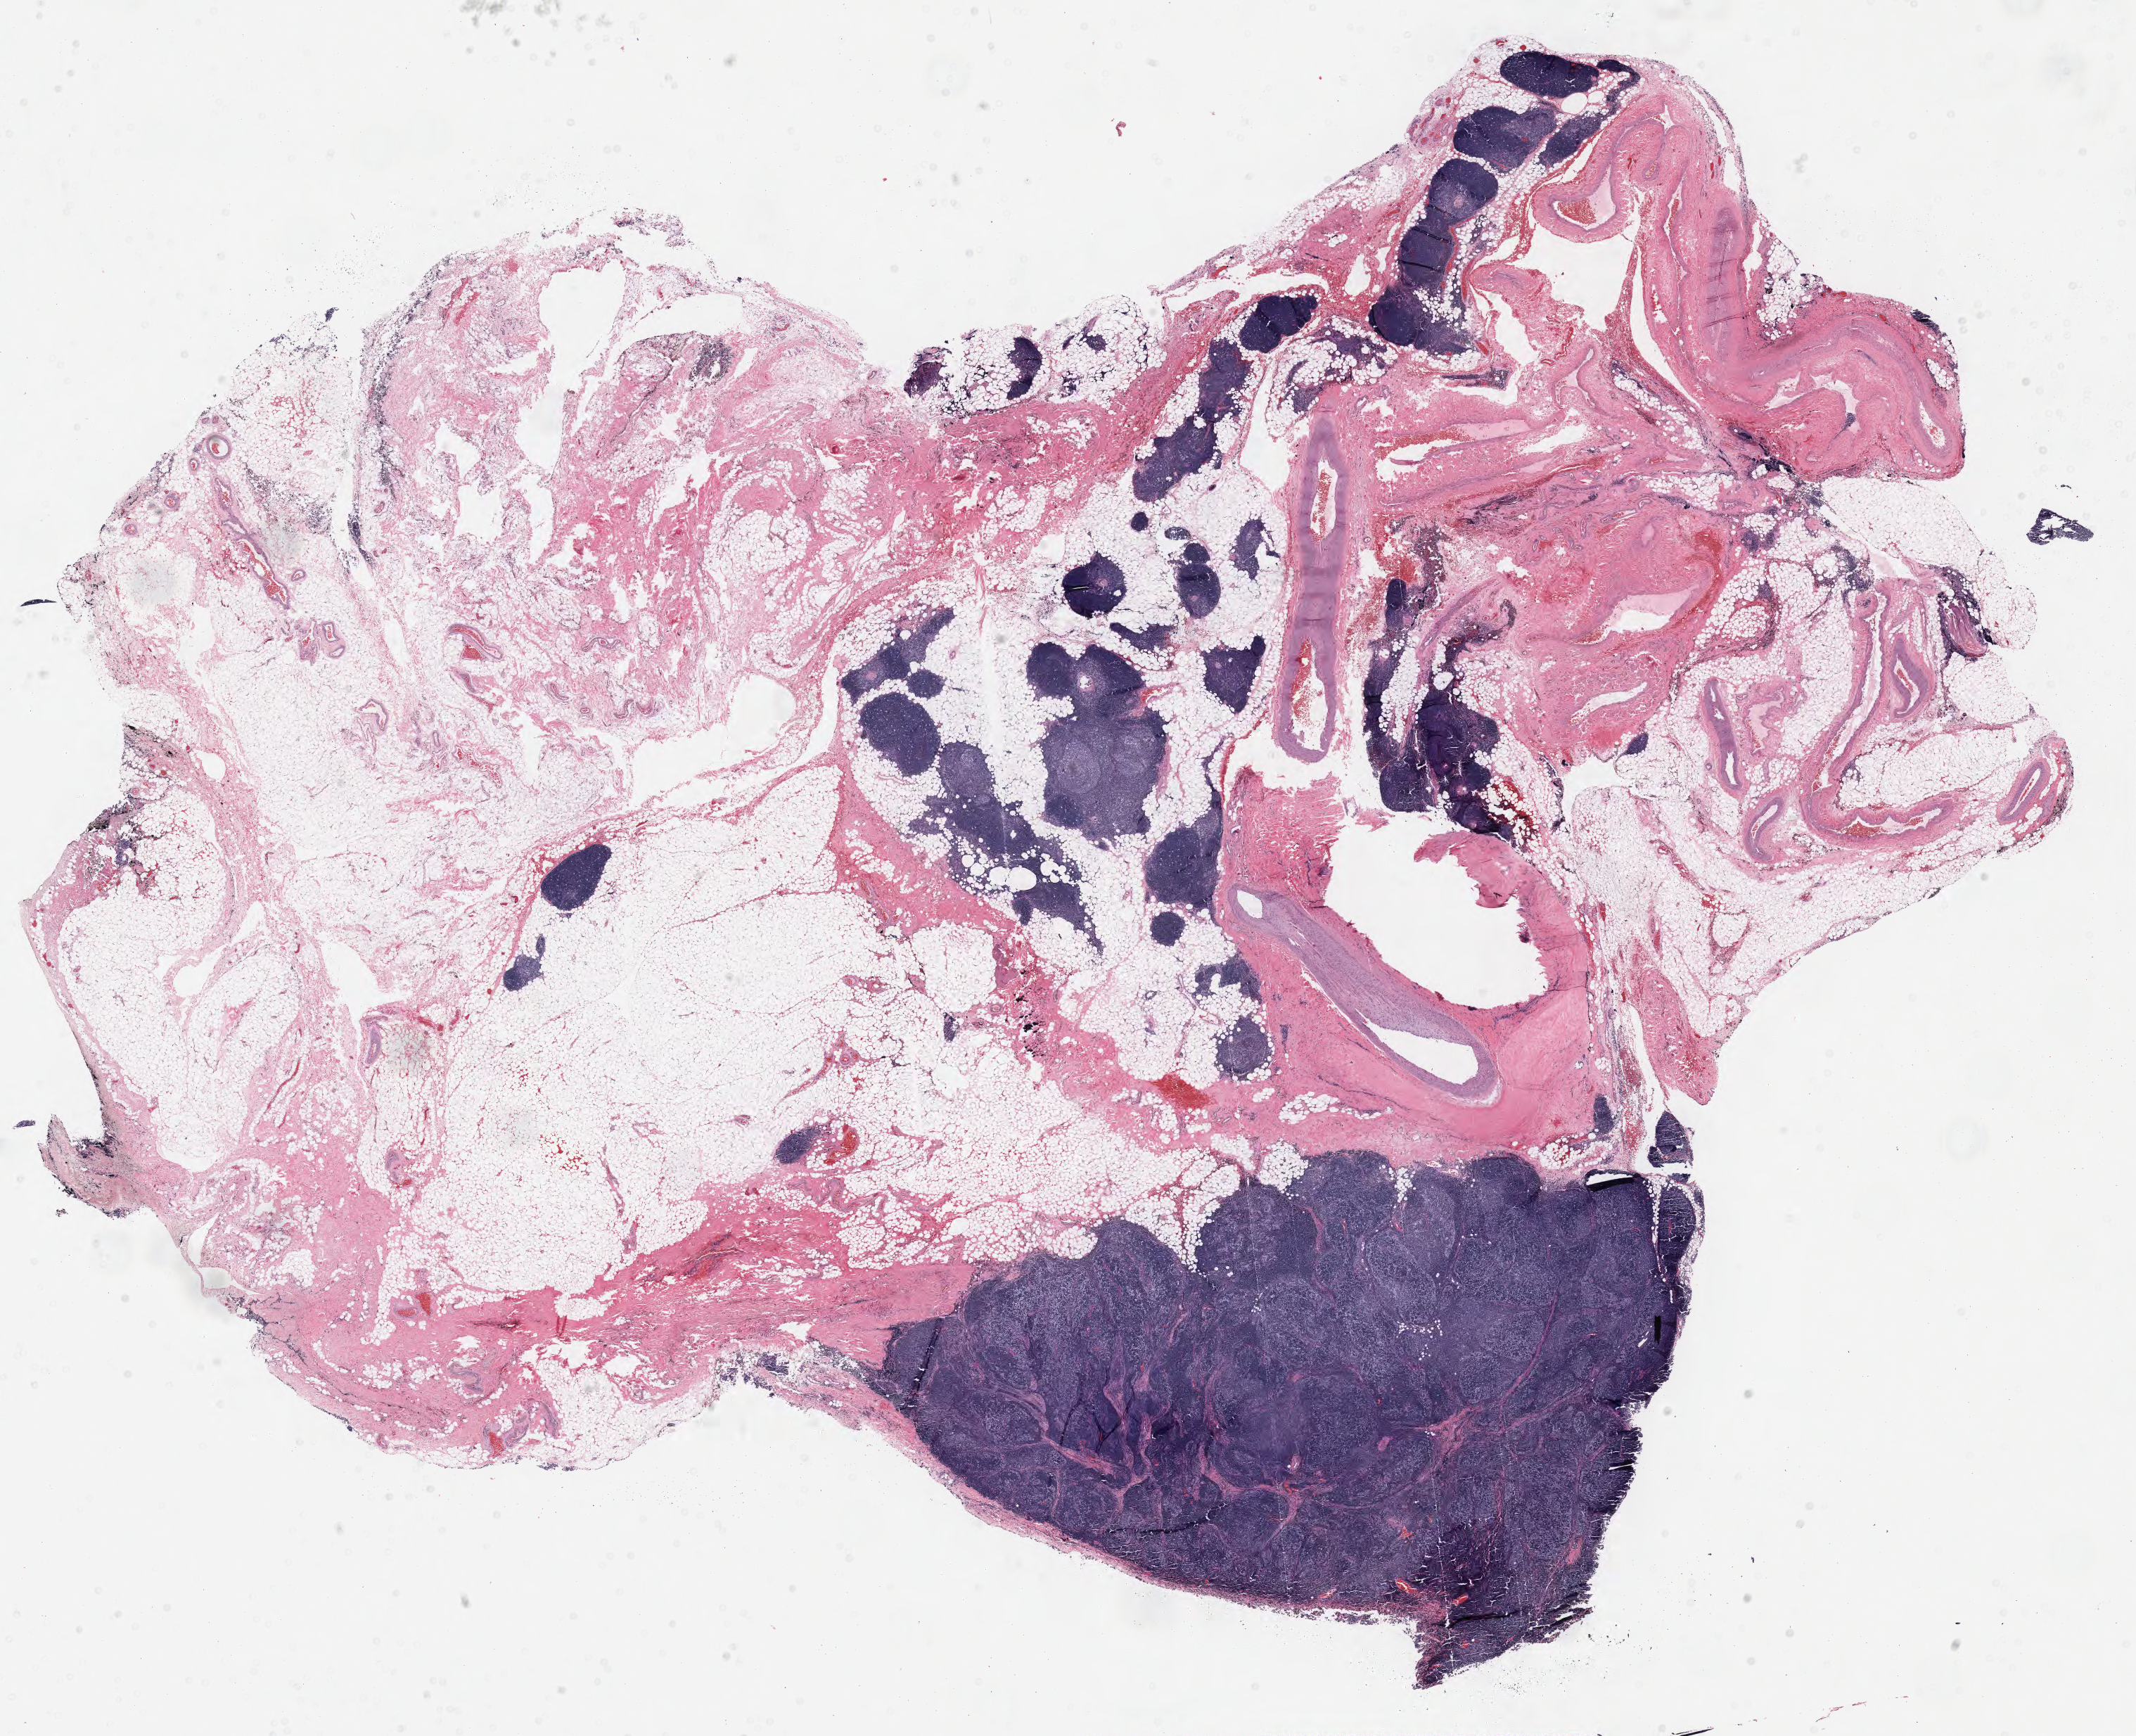
Digitized H&E tissue section (whole slide) — a low-resolution overview of the entire scanned area, about 24.1 x 19.6 mm (from a 40x scan); formalin-fixed paraffin-embedded (FFPE) diagnostic section; sample: primary tumour, thymus. Male, age 44 years at initial diagnosis.
Diagnosis: Thymoma, type B2, malignant.